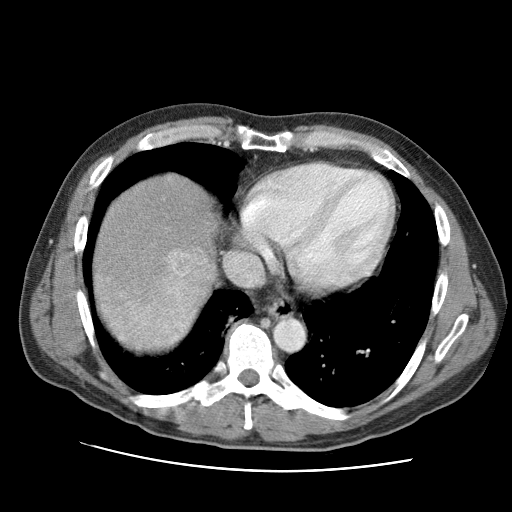
Contrast-enhanced abdominal CT (liver protocol), one axial slice; reconstruction kernel STANDARD; one of 2 acquisitions stored at this slice position; soft-tissue window (W 400 / L 40 HU); 2.5 mm slice thickness; 512 × 512 image matrix, field of view 360 × 360 mm. Case-level facts recorded for this patient, not image findings: diagnosis: hepatocellular carcinoma (patient treated with transarterial chemoembolisation; whether this scan precedes or follows treatment is not stated here); TNM stage (as recorded): Stage-IVA; Child-Pugh class: A; tumour nodularity: multinodular.
Structures marked on this image (semi-automatically segmented with operator editing):
- liver parenchyma outside the tumour (the mass and vessels are separate outlines, so this box may not span the whole liver): bounding box (x1, y1, x2, y2) in pixels: (94, 174, 218, 328)
- mass: (95, 246, 214, 354)
- liver vessels: (132, 286, 195, 326)